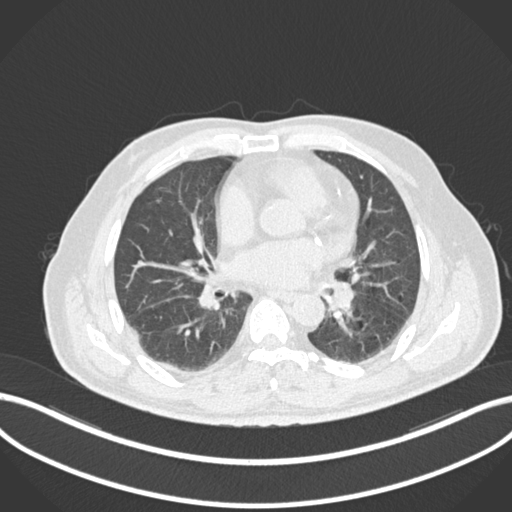
Chest CT, one axial slice; reconstruction kernel B30f; lung window (W 1500 / L -600 HU); 512 × 512 image matrix, field of view 400 × 400 mm. Patient: male, 71 years. Case-level facts recorded for this patient, not image findings: clinical TNM (as recorded): T1b N0 M0.
Annotated regions visible in this slice (rectangle marked by the reading radiologist):
- lung tumour (recorded histology: squamous cell carcinoma): box from (x=330, y=279) to (x=357, y=318) px